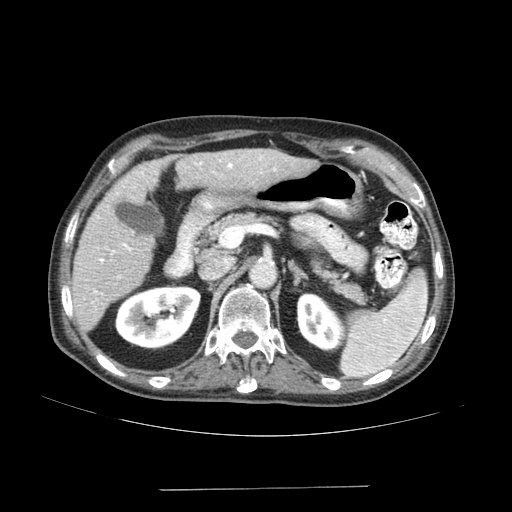
Contrast-enhanced abdominal CT (liver protocol), one axial slice; slice 84 of 192 in the series (ordered by position); 120 kVp; soft-tissue window (W 400 / L 40 HU); 512 × 512 image matrix, field of view 400 × 400 mm. From the clinical record (not read from this slice): diagnosis: hepatocellular carcinoma (patient treated with transarterial chemoembolisation; whether this scan precedes or follows treatment is not stated here); TNM stage (as recorded): Stage-IVA; Child-Pugh class: A.
Annotated regions visible in this slice (semi-automatic segmentation, software-assisted and operator-edited):
- liver parenchyma outside the tumour (the mass and vessels are separate outlines, so this box may not span the whole liver): box from (x=72, y=148) to (x=316, y=330) px
- liver vessels: (x=94, y=156)–(x=276, y=293)